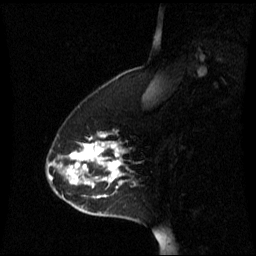
Breast MRI (dynamic contrast-enhanced), one sagittal slice; position 17 of 60 along the scan axis; dynamic contrast-enhanced series, image 2 of 3 at this slice position (ordered by acquisition); 1.5 T; TE 4.2 ms, TR 8.4 ms; 2.2 mm slice thickness; 256 × 256 image matrix. Female patient, age 45 years. From the clinical record (not read from this slice): setting: breast cancer imaged before/during neoadjuvant chemotherapy; receptor status: HR-positive, HER2-negative.
Outlined on this slice (semi-automatic segmentation, software-assisted and operator-edited):
- analysis volume of interest (the breast-tissue region the enhancement analysis was run in; not a lesion): box from (x=46, y=132) to (x=137, y=221) px
- tumour enhancement mask (voxels above the 70 % enhancement threshold inside the analysis volume of interest): (x=48, y=134)–(x=123, y=197)